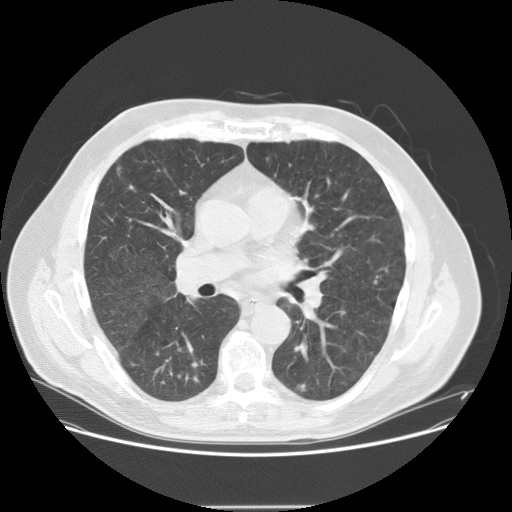
Low-dose screening chest CT, one axial slice; slice 80 of 143 in the series (ordered by position); reconstruction kernel STANDARD; 120 kVp; lung window (W 1500 / L -600 HU); 2.5 mm slice thickness; 512 × 512 image matrix.
Annotated regions visible in this slice (manually delineated by an expert):
- lesion 5 (tumor): bounding box [x1, y1, x2, y2] px = [298, 383, 306, 392]